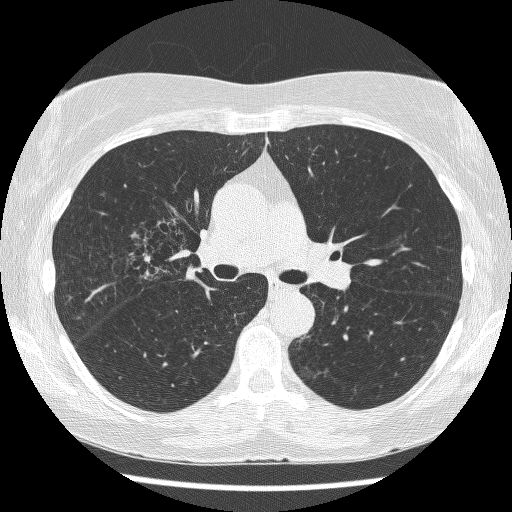
Low-dose screening chest CT, axial slice. First (baseline) screen. Lung window (W 1500 / L -600 HU). 1.25 mm slice thickness. 120 kVp. Slice 169 of 271 in the series. 512 × 512 image matrix. Female, age 64 years at enrolment. Former smoker at enrolment.
Expert reader's lesion annotation, box from (x=123, y=217) to (x=200, y=282) px. The screening reader recorded 3 non-calcified nodules or masses ≥4 mm on this exam (right upper lobe, right upper lobe, left lower lobe); which of them this box marks is not recorded. Lung cancer was diagnosed 735 days after this screen (after the third annual screen): adenocarcinoma, NOS, right upper lobe, right middle lobe, right hilum, stage IV (AJCC 6th edition), 85 mm at pathology.